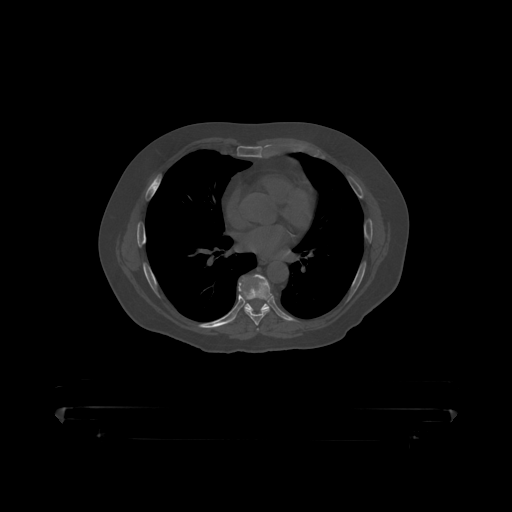
CT including the spine, one axial slice; slice 271 of 390 in the series (ordered by position); reconstruction kernel STANDARD; bone window (W 1800 / L 400 HU); 1.25 mm slice thickness; 512 × 512 image matrix, field of view 650 × 650 mm. Patient: male, 60 years. Case-level facts recorded for this patient, not image findings: primary cancer: prostate.
Structures marked on this image (semi-automatic segmentation, software-assisted and operator-edited):
- T7 vertebra: bounding box [x1, y1, x2, y2] px = [239, 275, 272, 319]
- T8 vertebra: [245, 303, 270, 312]